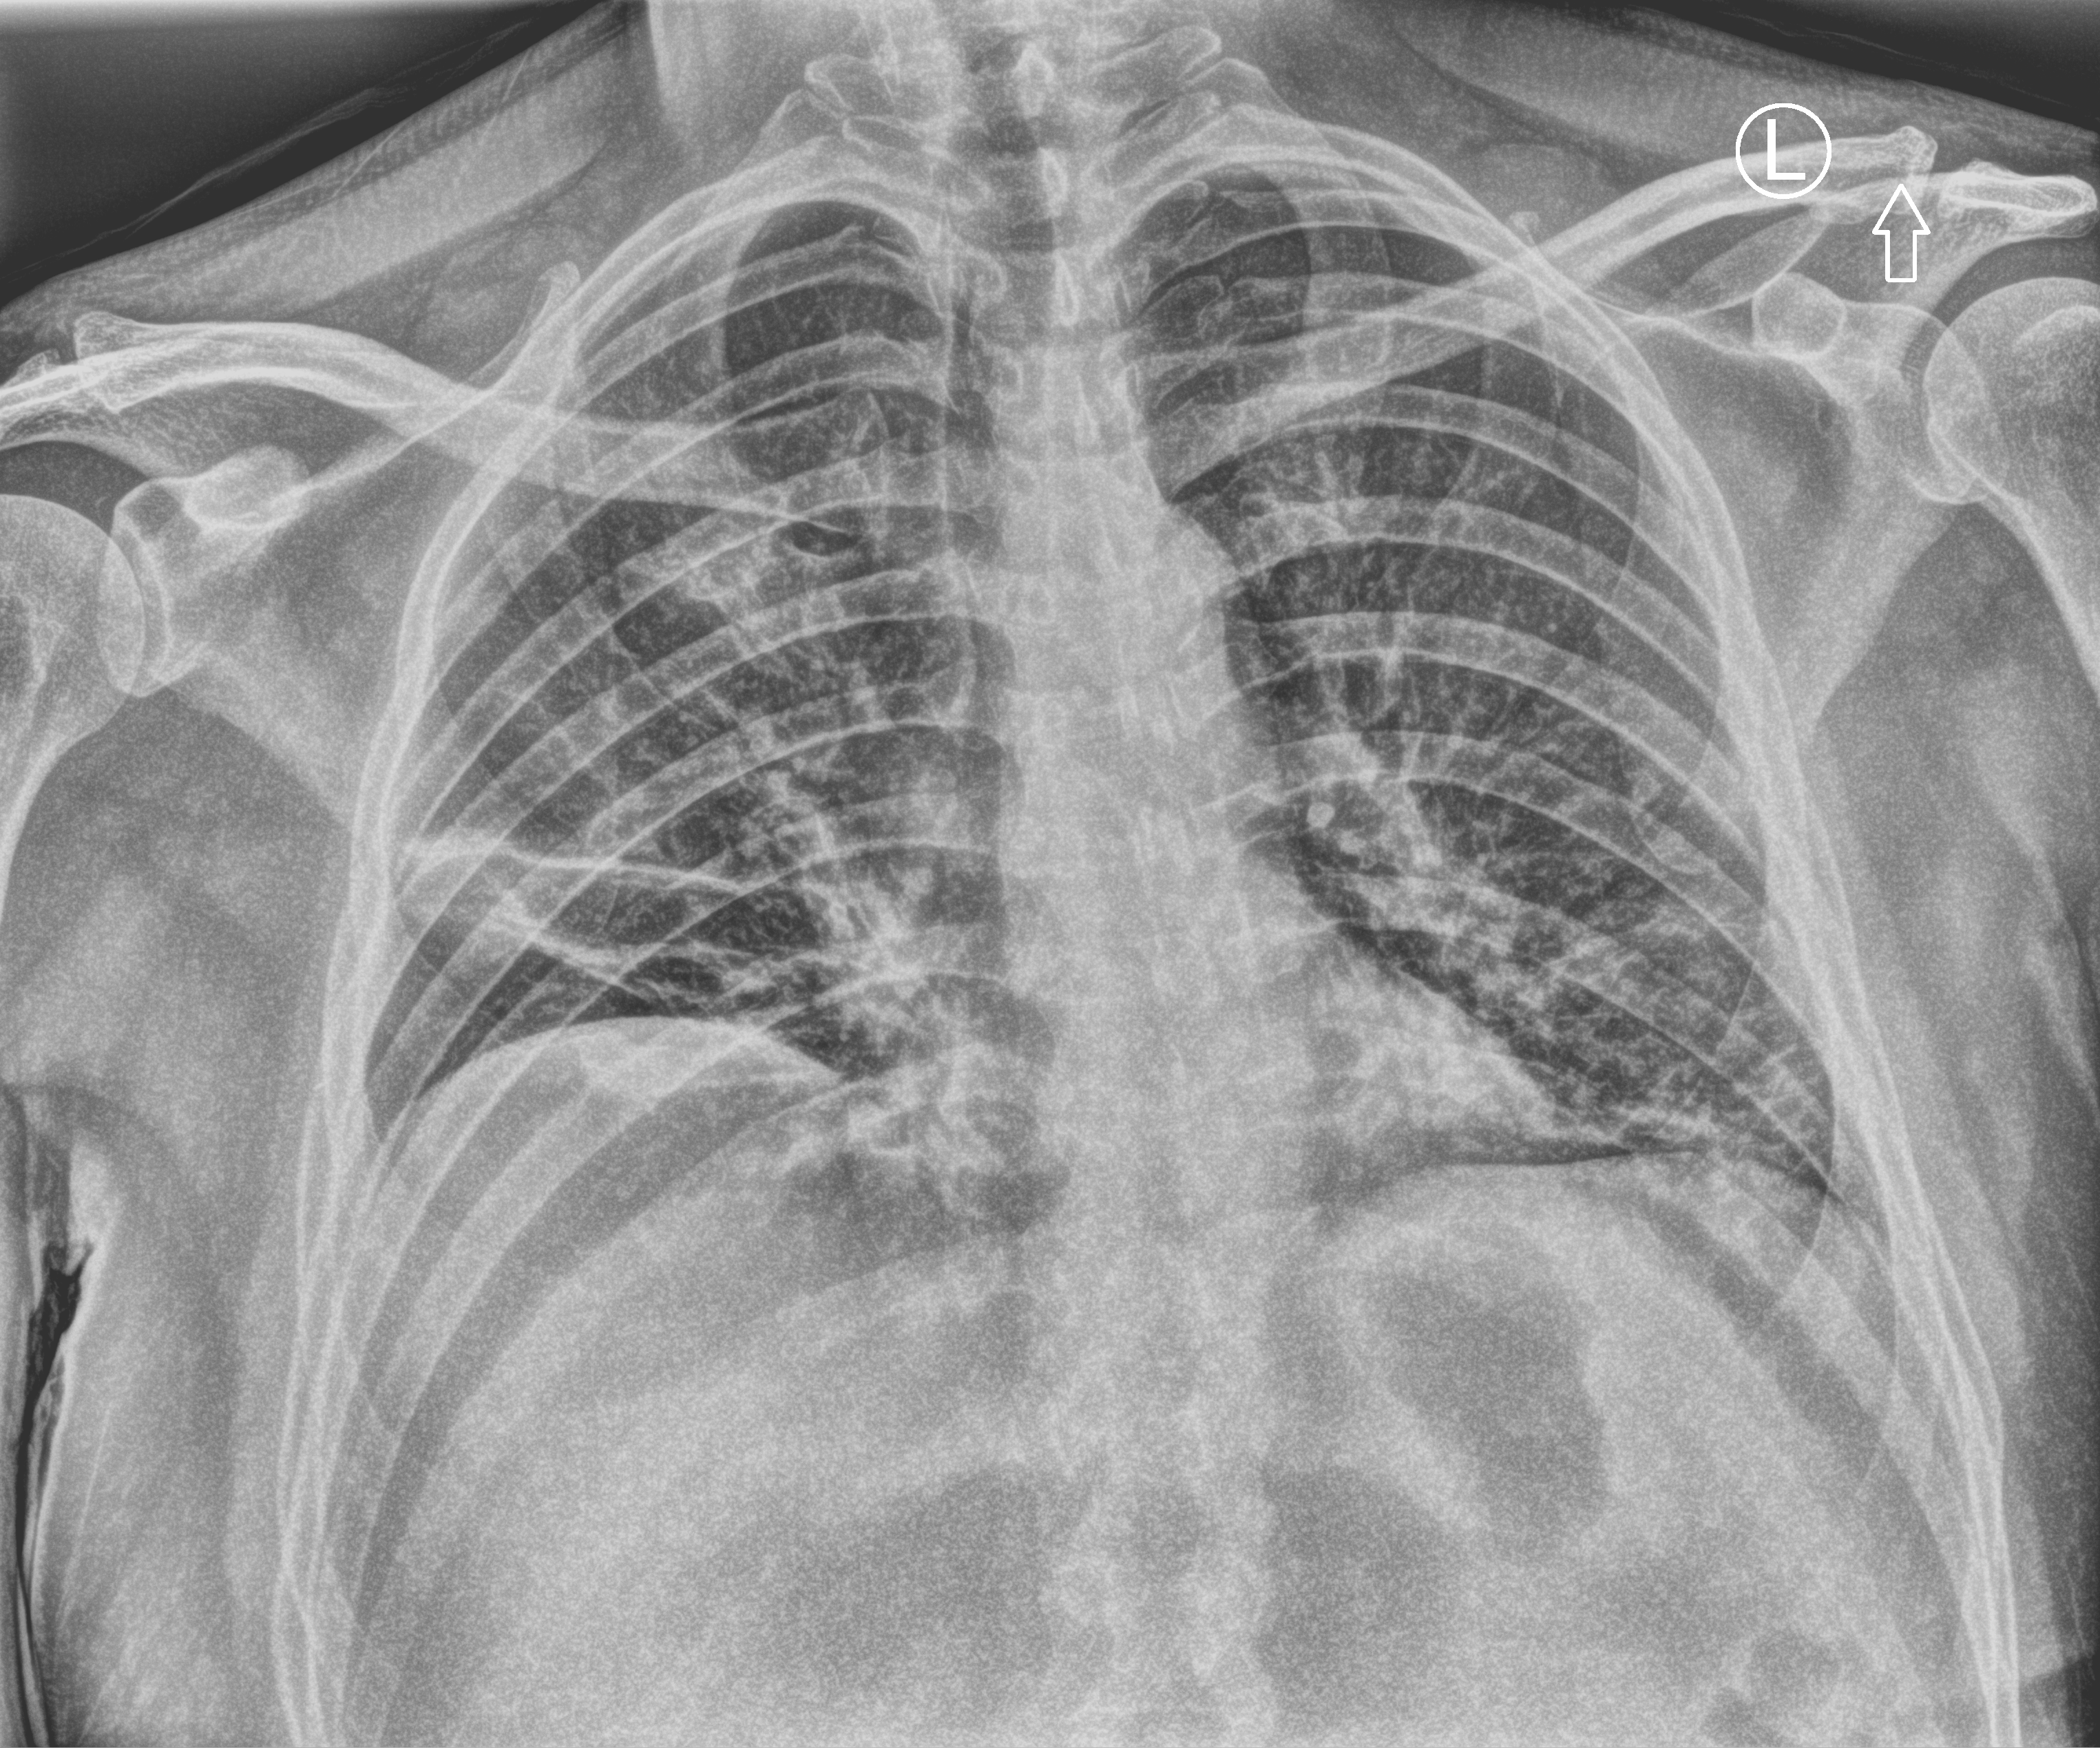
Chest X-ray (portable); anteroposterior (AP) projection. Patient hospitalised with COVID-19; male, aged 18–59 years.
Admission-level facts for this patient (not findings on this image; timing relative to this image not recorded): length of hospital stay: 10 days; admitted to intensive care during this hospital stay: no; diabetes (admission record): yes.